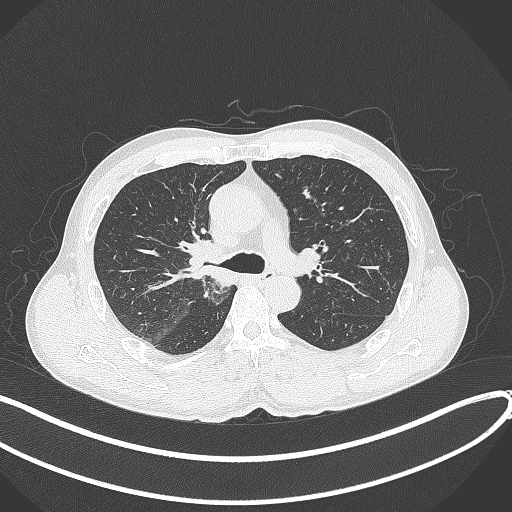
Chest CT, one axial slice. Slice 253 of 409 in the series (ordered by position). Reconstruction kernel B70f. Lung window (W 1500 / L -600 HU). 1 mm slice thickness. 512 × 512 image matrix, field of view 400 × 400 mm. Male patient, age 53 years. Case-level facts recorded for this patient, not image findings: clinical TNM (as recorded): T1b N0 M0.
Annotated regions visible in this slice (rectangle marked by the reading radiologist):
- lung tumour (recorded histology: squamous cell carcinoma): box from (x=180, y=237) to (x=229, y=286) px